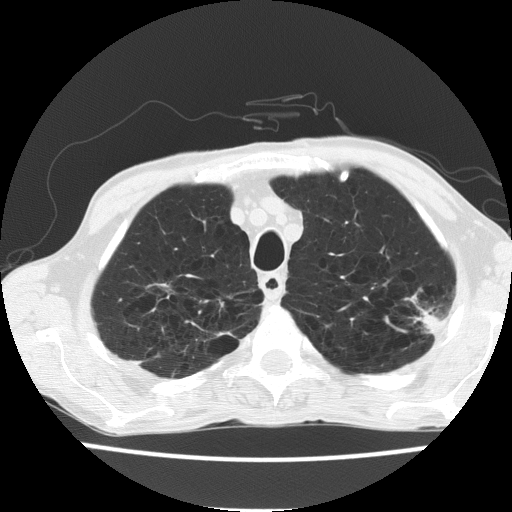
Low-dose screening chest CT, axial slice, baseline annual screen, lung window (W 1500 / L -600 HU), 2 mm slice thickness, slice 34 of 187 in the series, 512 × 512 image matrix, field of view 320 × 320 mm. Male, age 60 years at enrolment. Current smoker at enrolment.
• Lesion marked by an expert reader, bounding box [x1, y1, x2, y2] px = [396, 286, 458, 348].
• Screening reader's record for this exam: no non-calcified nodule ≥4 mm recorded.